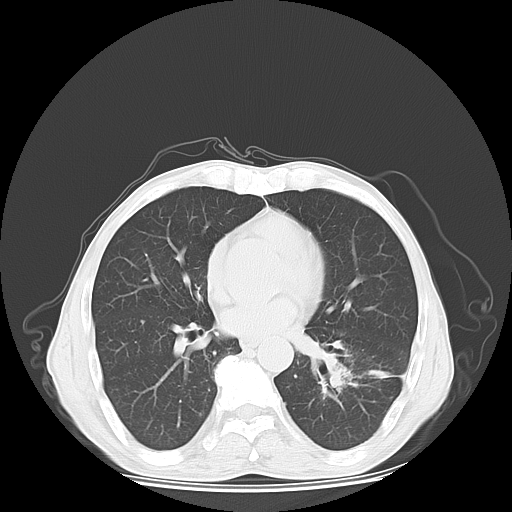
Chest CT, one axial slice. Position 30 of 65 along the scan axis. Reconstruction kernel LUNG. Lung window (W 1500 / L -600 HU). 512 × 512 image matrix. Patient: male, 63 years. Case-level facts recorded for this patient, not image findings: clinical TNM (as recorded): T1c N0 M1b.
Annotated regions visible in this slice (rectangle marked by the reading radiologist):
- lung tumour (recorded histology: adenocarcinoma): bounding box <301,343,365,401> (left, top, right, bottom; pixels)